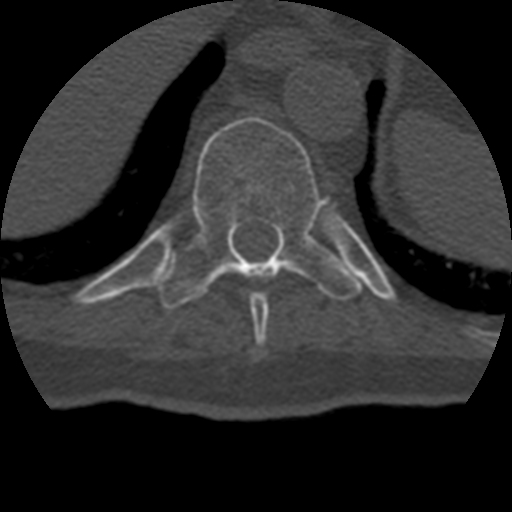
CT including the spine, one axial slice. Slice 224 of 399 in the series (ordered by position). 120 kVp. Bone window (W 1800 / L 400 HU). 1.25 mm slice thickness. 512 × 512 image matrix, field of view 160 × 160 mm. Patient age 69 years. From the clinical record (not read from this slice): primary cancer: prostate.
Outlined on this slice (semi-automatic segmentation, software-assisted and operator-edited):
- T10 vertebra: bounding box <158,117,362,309> (left, top, right, bottom; pixels)
- T9 vertebra: <250,292,269,347>